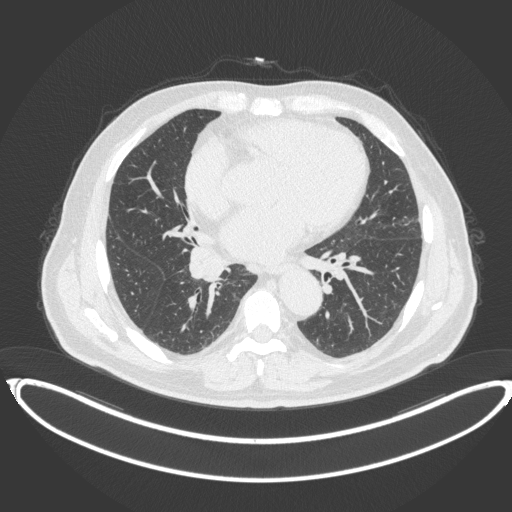
Chest CT, one axial slice; slice 190 of 383 in the series (ordered by position); 120 kVp; lung window (W 1500 / L -600 HU); 512 × 512 image matrix, field of view 448 × 448 mm. Male patient, age 61 years. Case-level facts recorded for this patient, not image findings: clinical TNM (as recorded): T1b N1 M0.
Structures marked on this image (bounding box drawn by a radiologist):
- lung tumour (recorded histology: squamous cell carcinoma): bounding box <188,242,229,286> (left, top, right, bottom; pixels)